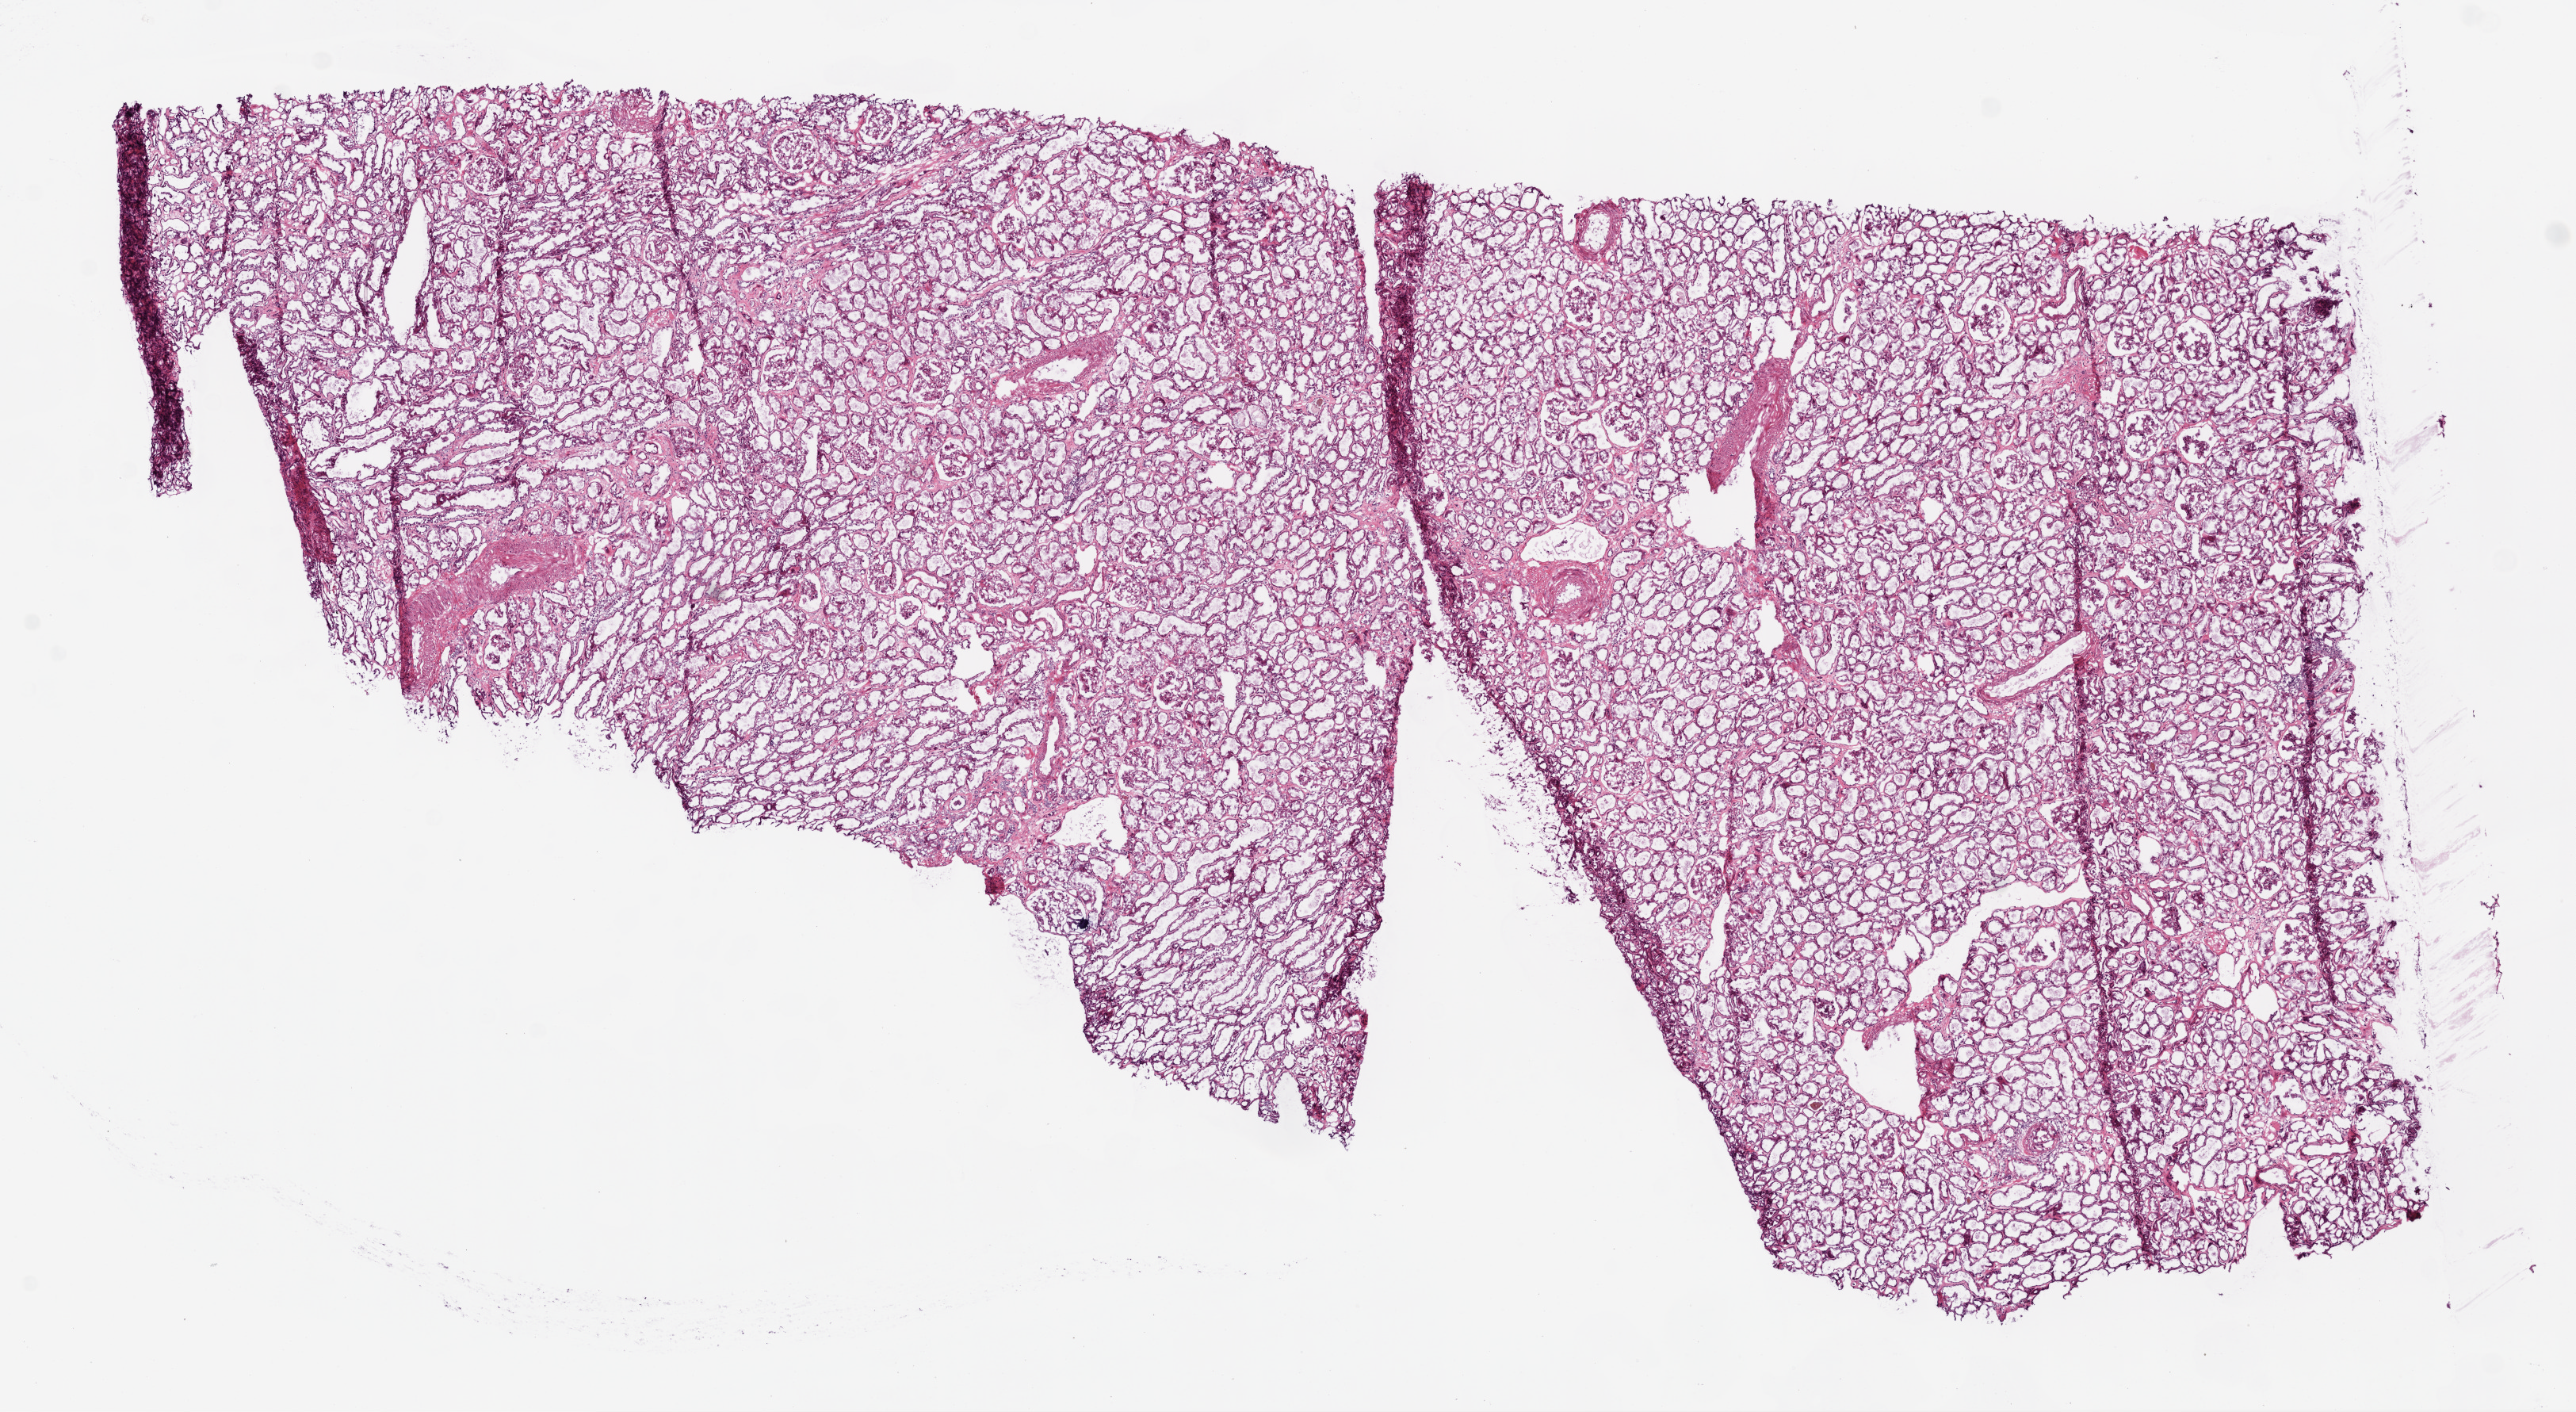
Digitized H&E-stained tissue section (whole slide), whole scanned area (about 13.0 x 7.1 mm, slide scanned at 20x) shown as a low-resolution overview, frozen section, sample: solid tissue normal (non-tumour tissue), kidney. Patient: male, age at initial diagnosis 74 years.
* this section: solid tissue normal sample (biorepository sample class)
* patient diagnosis: Clear cell adenocarcinoma, NOS